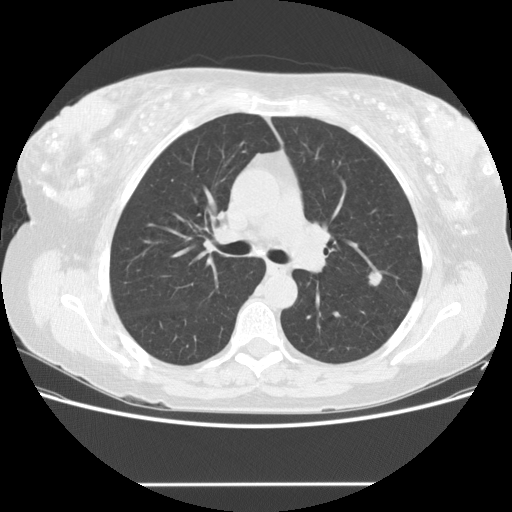
Low-dose screening chest CT, one axial slice. Slice 97 of 151 in the series (ordered by position). Reconstruction kernel STANDARD. 120 kVp. Lung window (W 1500 / L -600 HU). 2.5 mm slice thickness. 512 × 512 image matrix, field of view 360 × 360 mm.
Outlined on this slice (expert manual segmentation):
- lesion 1 (tumor, upper lobe of left lung): bounding box <368,271,382,286> (left, top, right, bottom; pixels)